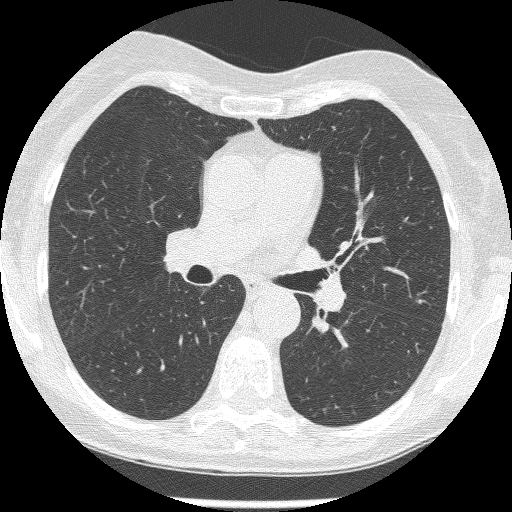
Axial slice from a low-dose chest CT screening exam; second screening round (one year after baseline); lung window (W 1500 / L -600 HU); 1.25 mm slice thickness; lung (sharp) reconstruction kernel (BONE); slice 163 of 250 in the series. Female participant, aged 60 years at enrolment. Current smoker at enrolment.
Expert reader's lesion annotation, bounding box [x1, y1, x2, y2] px = [402, 287, 439, 315]. The screening reader recorded 2 non-calcified nodules or masses ≥4 mm on this exam (left upper lobe, left upper lobe); which of them this box marks is not recorded.